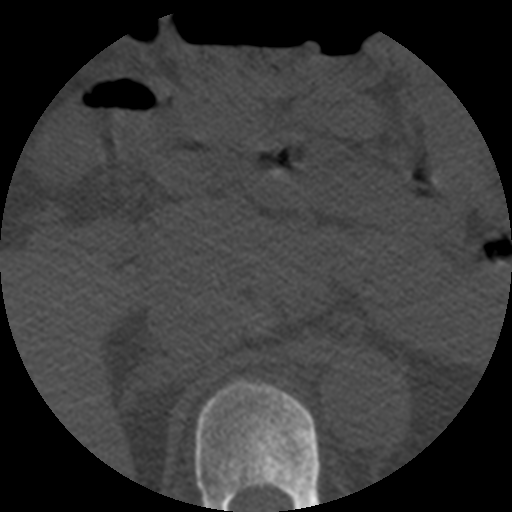
CT including the spine, one axial slice. Position 240 of 508 along the scan axis. Reconstruction kernel STANDARD. 120 kVp. Bone window (W 1800 / L 400 HU). 1.25 mm slice thickness. 512 × 512 image matrix, field of view 160 × 160 mm. Patient age 57 years. Case-level facts recorded for this patient, not image findings: primary cancer: prostate.
Annotated regions visible in this slice (semi-automatically segmented with operator editing):
- T11 vertebra: bounding box (x1, y1, x2, y2) in pixels: (195, 381, 321, 512)